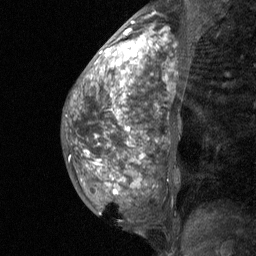
Breast MRI (dynamic contrast-enhanced), one sagittal slice; position 26 of 64 along the scan axis; dynamic contrast-enhanced study with each time point stored as its own series, time point 2 of 3 at this slice position (early post-contrast, ordered by acquisition time); 1.5 T; TE 4.8 ms, TR 27 ms; 2 mm slice thickness; 256 × 256 image matrix, field of view 180 × 180 mm. Patient: female, 36 years. From the clinical record (not read from this slice): setting: breast cancer imaged before/during neoadjuvant chemotherapy; receptor status: HR-positive, HER2-negative.
Outlined on this slice (semi-automatically segmented with operator editing):
- analysis volume of interest (the breast-tissue region the enhancement analysis was run in; not a lesion): bounding box (x1, y1, x2, y2) in pixels: (67, 12, 190, 237)
- tumour enhancement mask (voxels above the 90 % enhancement threshold inside the analysis volume of interest): (87, 22, 167, 194)